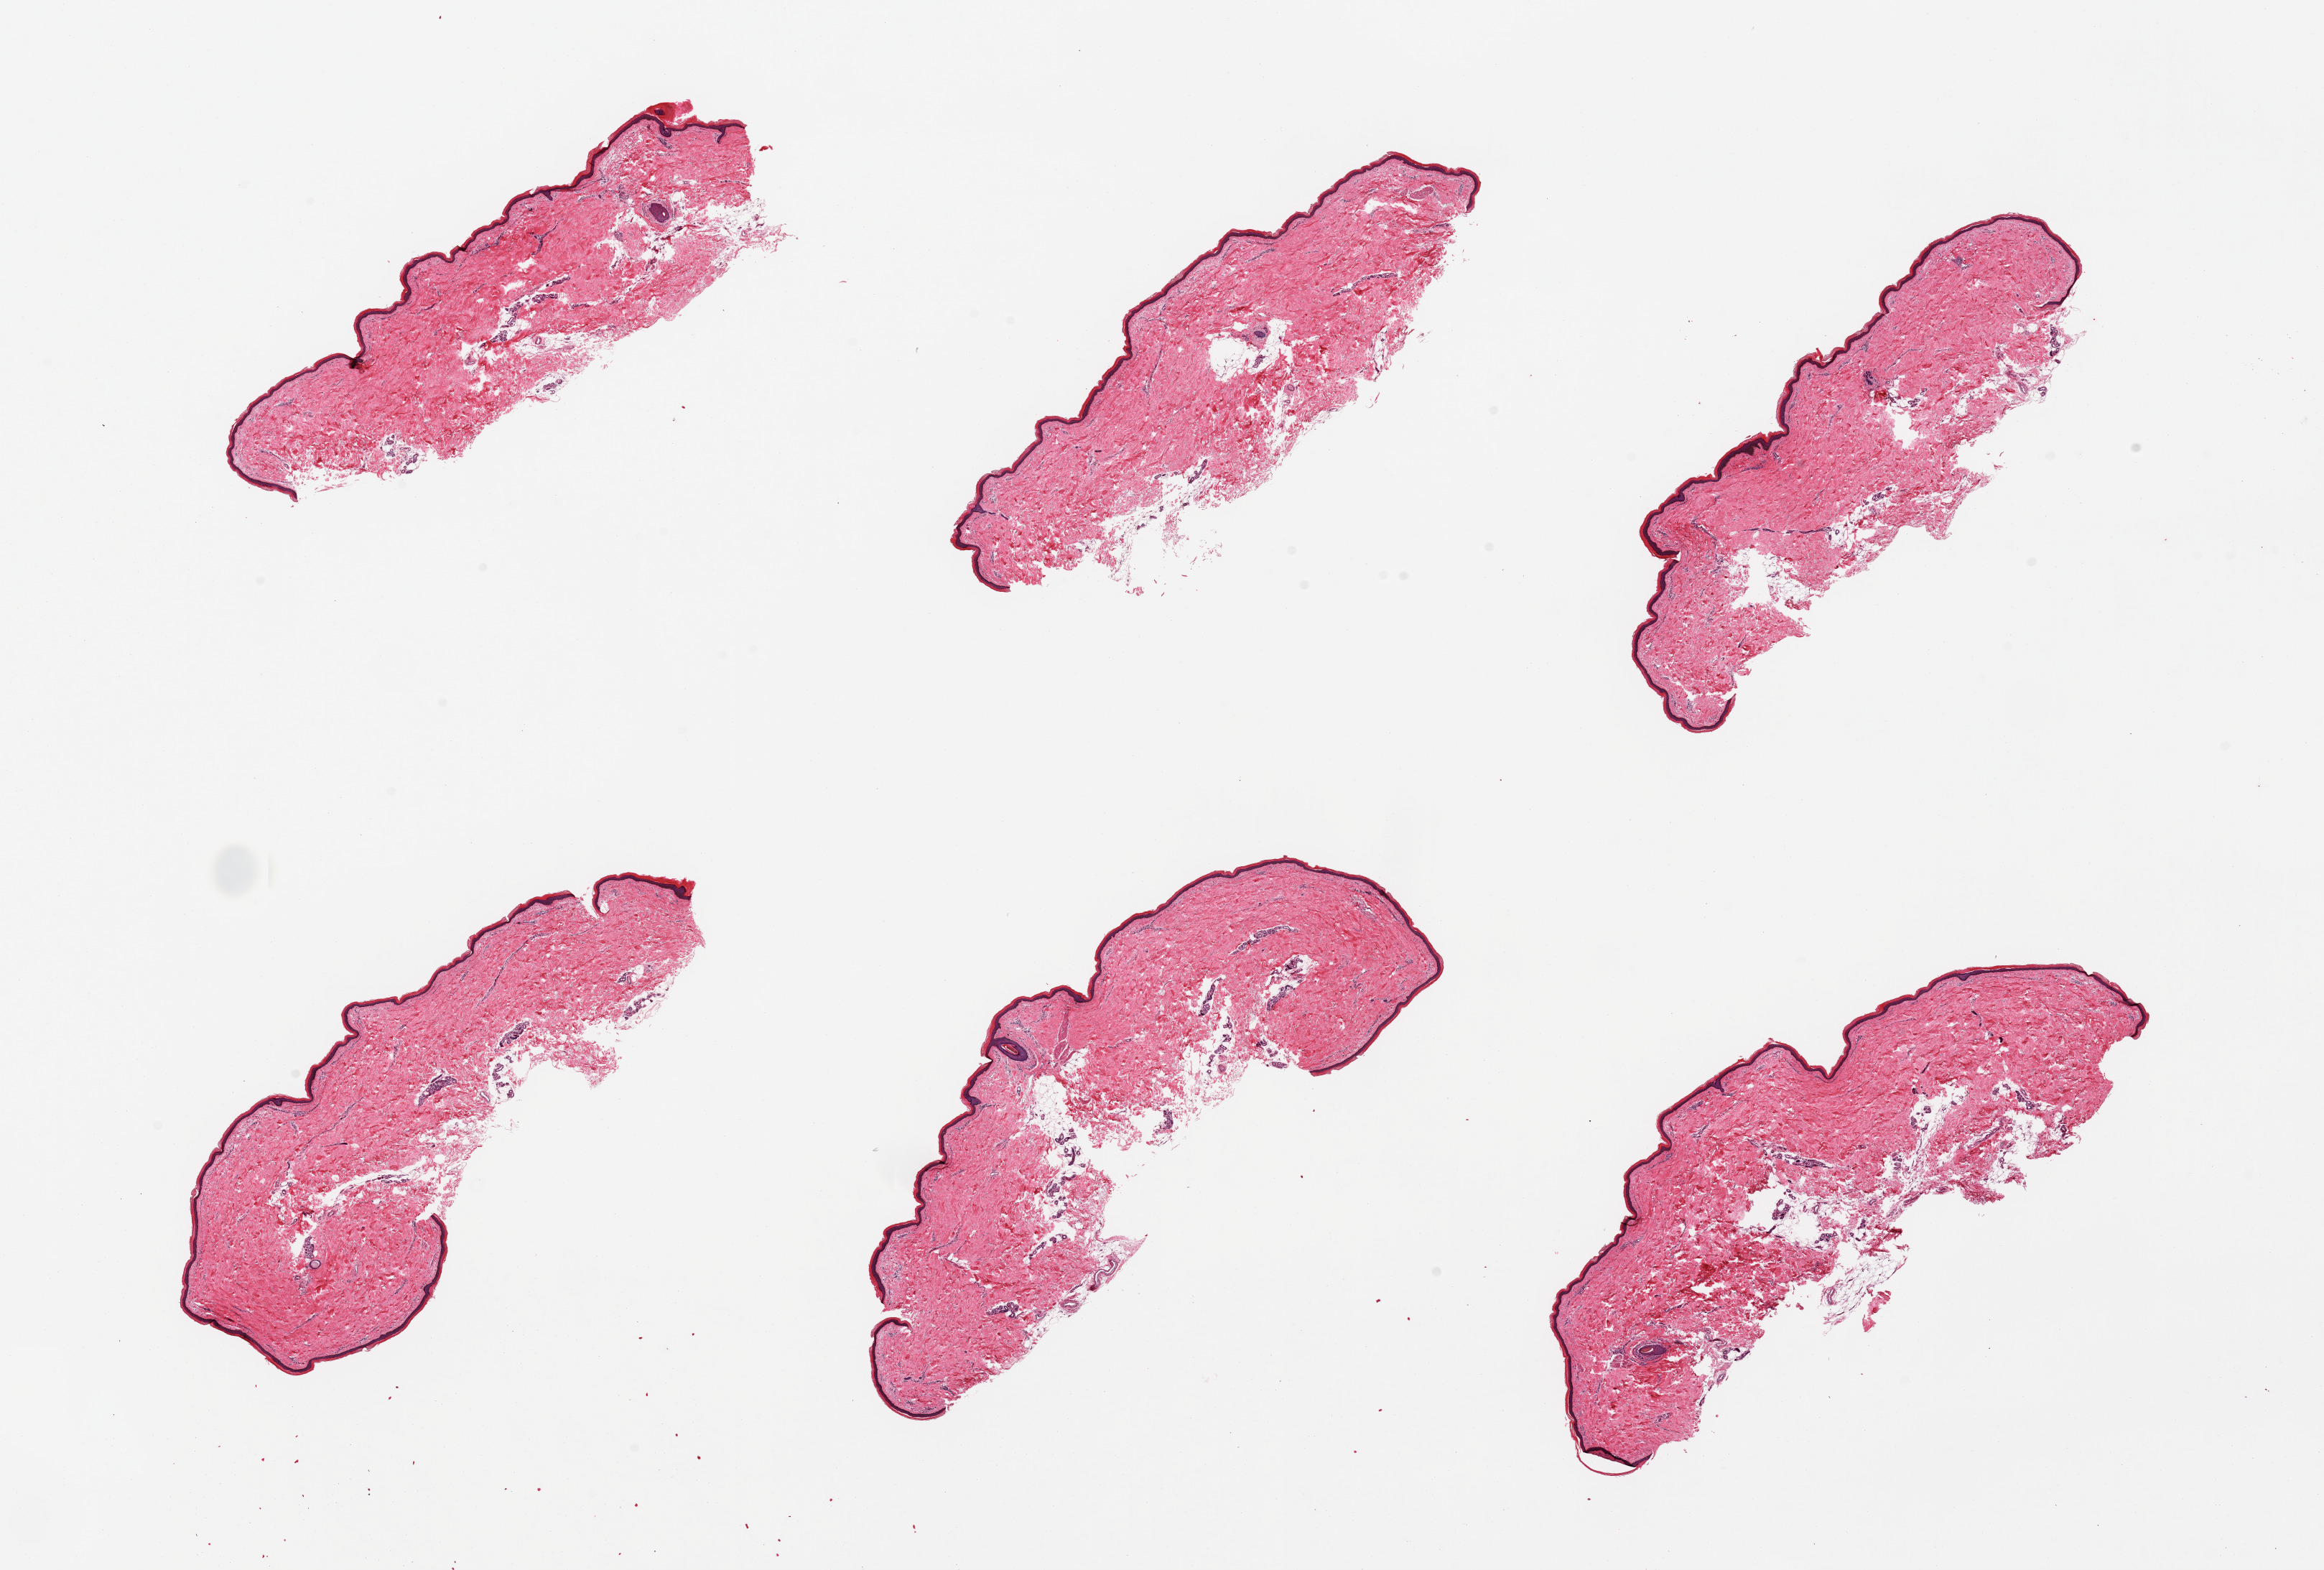
Hematoxylin and eosin (H&E) whole-slide image, brightfield, shown as a low-resolution overview of the whole scanned area (about 25.6 x 17.3 mm). PAXgene-fixed, paraffin-embedded tissue. Sampled site (target tissue): skin of lower leg. Tissue donor sample. Female donor.
* review note (as recorded): 6 pieces; well trimmed; 5% dermal fat